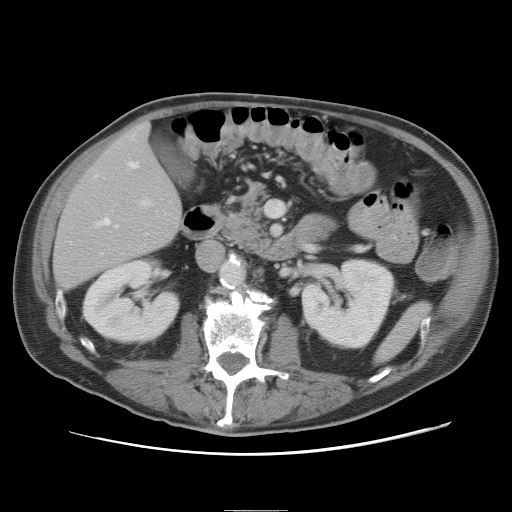
Contrast-enhanced abdominal CT, one axial slice; slice 27 of 89 in the series (ordered by position); 120 kVp; intravenous contrast given; soft-tissue window (W 400 / L 40 HU); 5 mm slice thickness; 512 × 512 image matrix, field of view 375 × 375 mm. Male patient, age 69 years. Case-level facts recorded for this patient, not image findings: diagnosis: colorectal cancer liver metastases, imaged before liver resection; multiple liver metastases: no; largest metastasis: 8.5 cm.
Annotated regions visible in this slice (outlined manually by an expert reader):
- hepatic veins: bounding box (x1, y1, x2, y2) in pixels: (96, 161, 139, 227)
- liver: (54, 123, 182, 290)
- planned liver remnant (the part of the liver to remain after resection): (54, 123, 182, 290)
- portal vein (with intrahepatic branches): (101, 199, 151, 254)